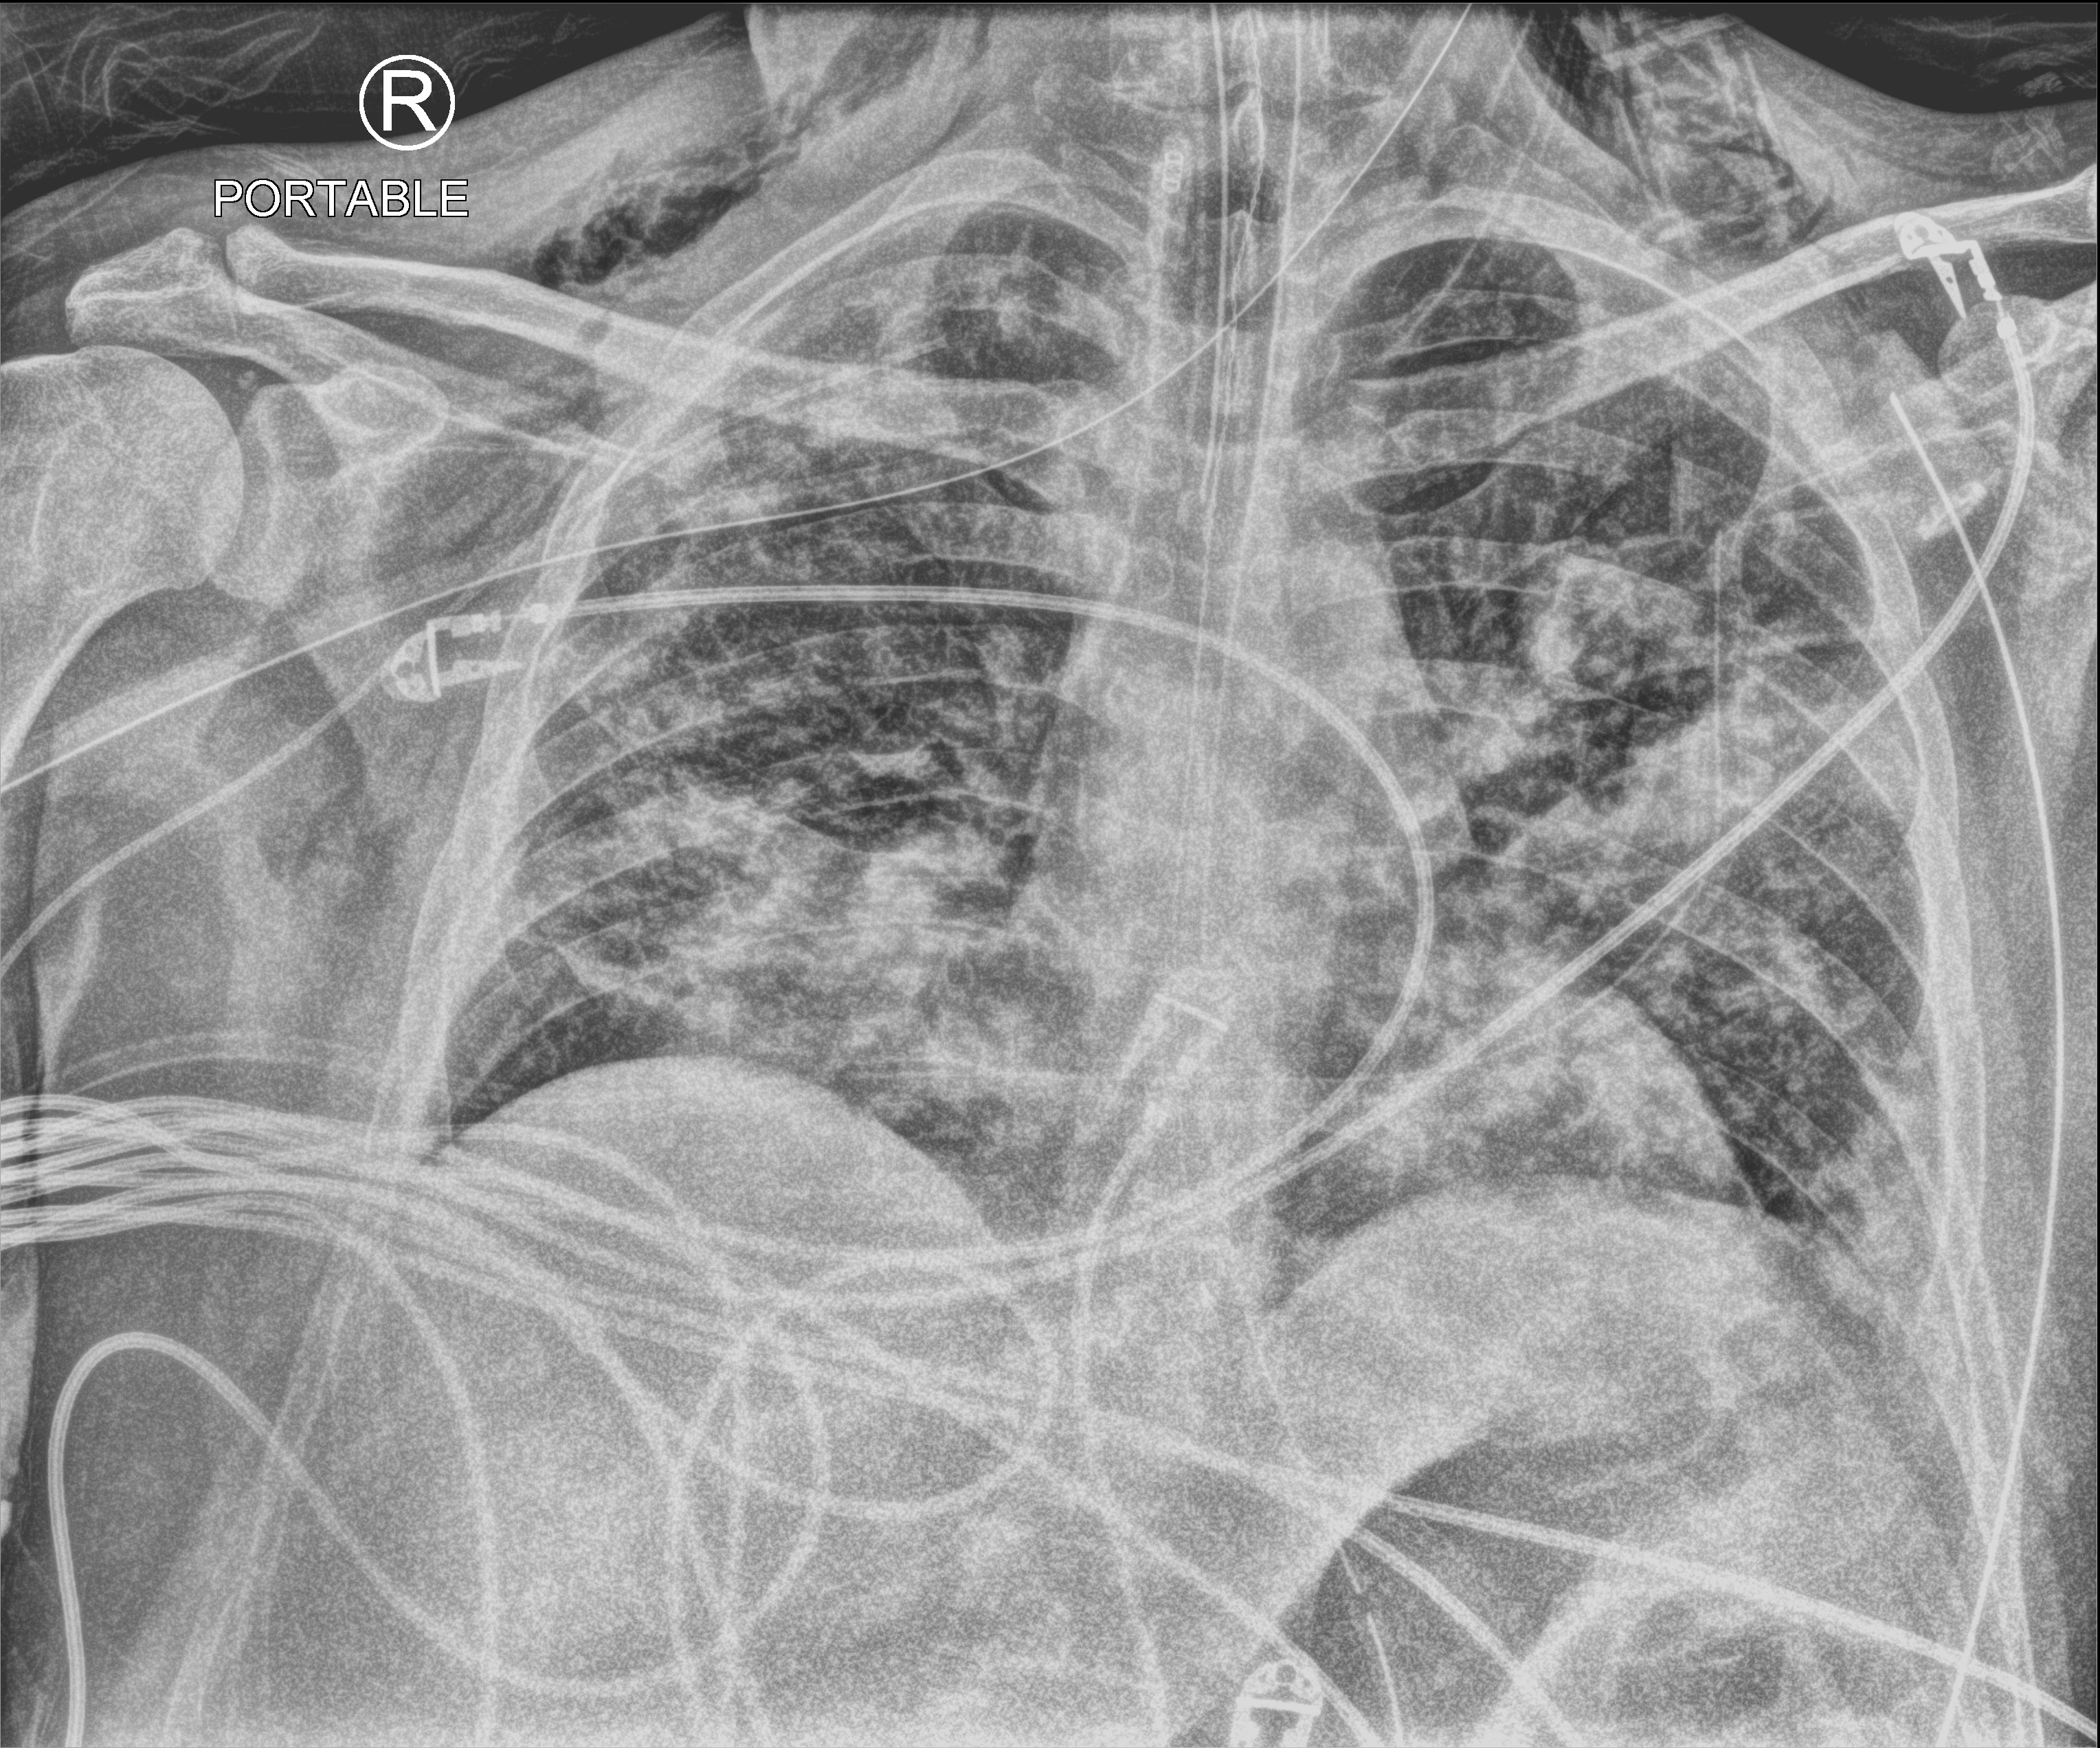
Chest X-ray (portable). Patient hospitalised with COVID-19, aged 18–59 years.
From the hospital-stay record, not from the radiograph (when in the stay this image was taken is not recorded):
- length of hospital stay: 50 days
- admitted to intensive care during this hospital stay: yes
- mechanically ventilated during this hospital stay: yes